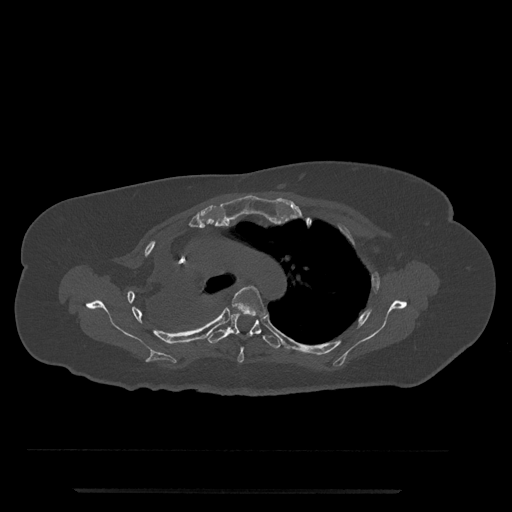
CT including the spine, one axial slice. Slice 564 of 797 in the series (ordered by position). Reconstruction kernel Br40s/3. 120 kVp. Bone window (W 1800 / L 400 HU). 0.5 mm slice thickness. 512 × 512 image matrix, field of view 440 × 440 mm. Patient: female, 51 years. From the clinical record (not read from this slice): primary cancer: neuro; vertebrae with lytic lesions (as recorded): T8.
Outlined on this slice (semi-automatically segmented with operator editing):
- T4 vertebra: bounding box <226,286,266,363> (left, top, right, bottom; pixels)
- T5 vertebra: <206,308,282,349>